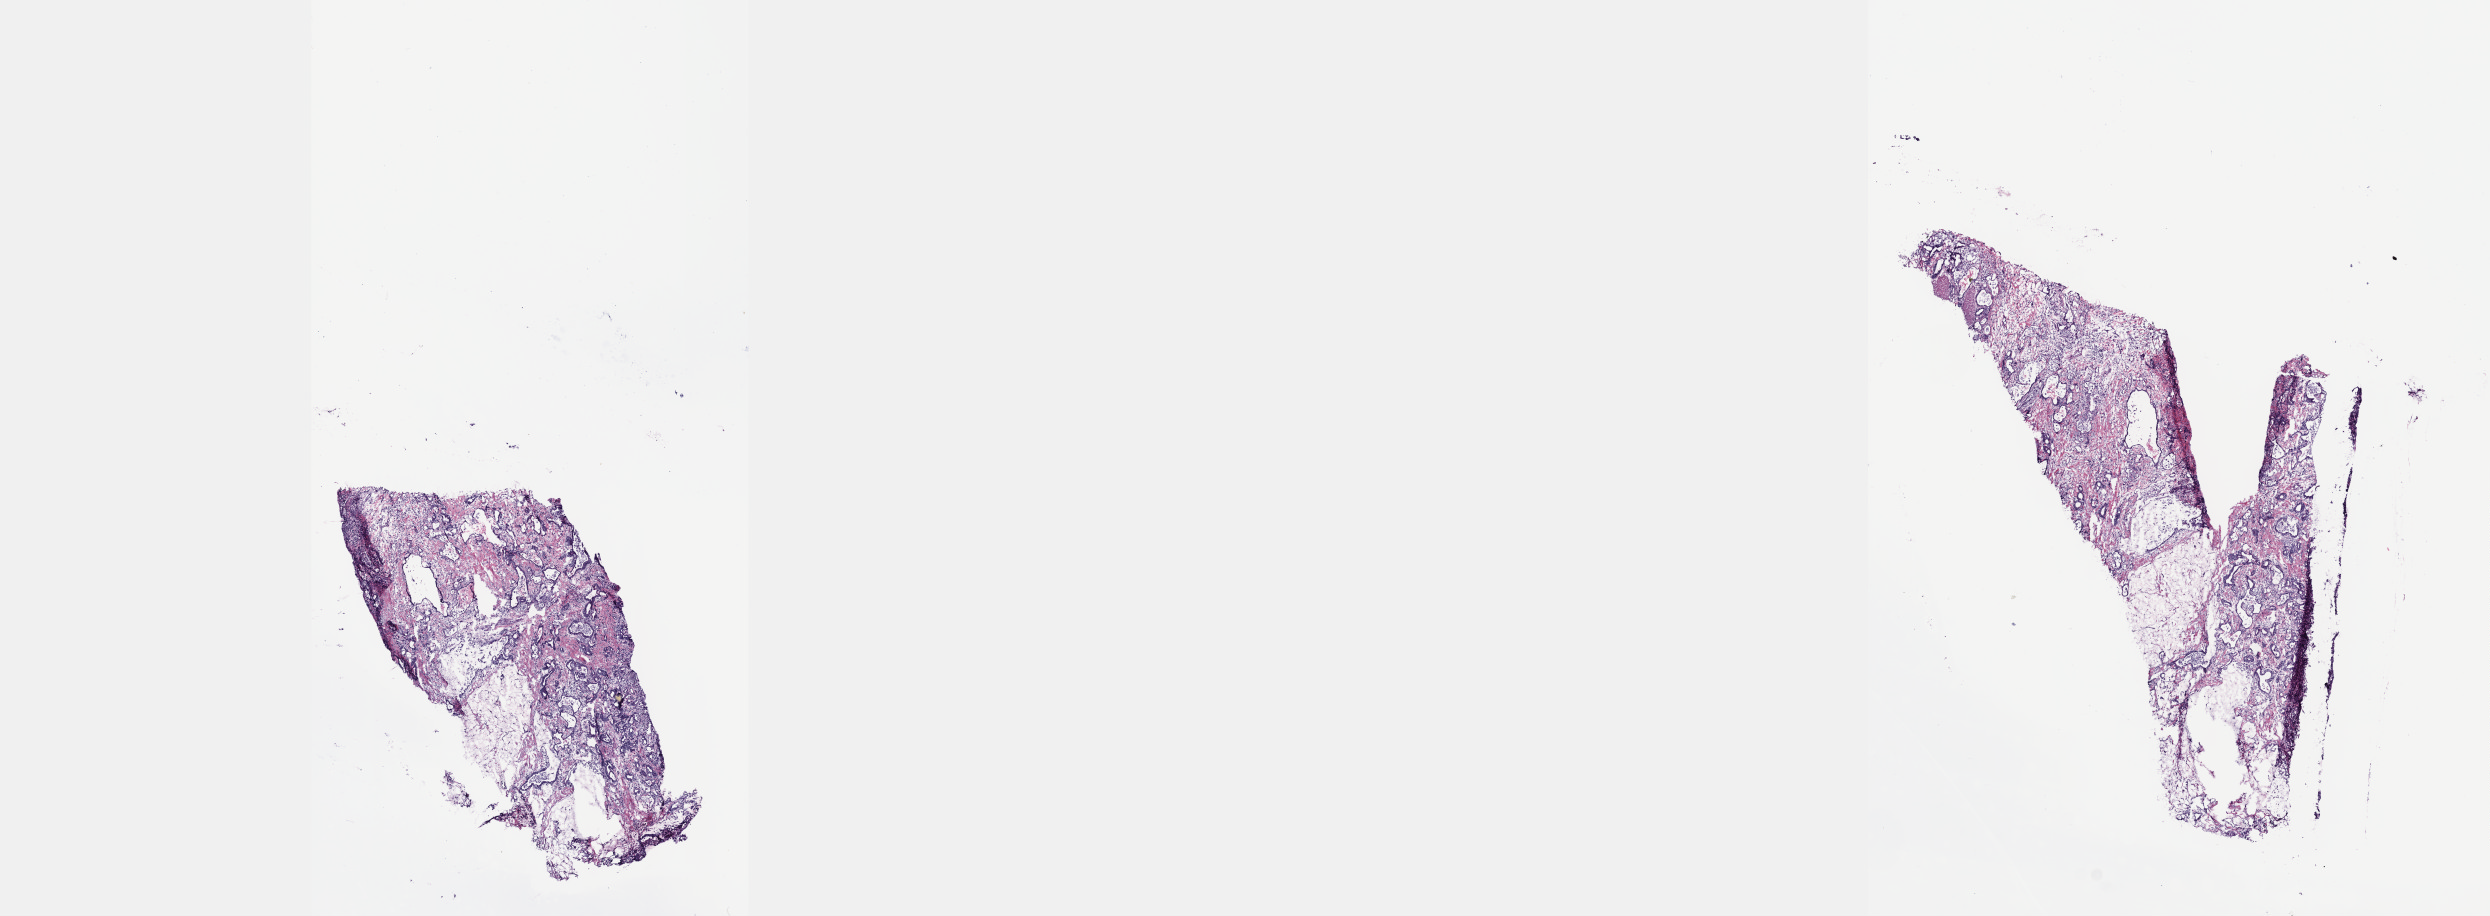
Whole-slide histology image, H&E-stained, whole scanned area (about 20.1 x 7.4 mm) shown as a low-resolution overview. Frozen section. Sample: primary tumour, stomach. Male patient; age at initial diagnosis 71 years. Histologic grade: G2 (moderately differentiated). Composition of this section per pathologist review: tumour cells 47%, tumour nuclei 80%, normal cells 0%, stromal cells 50%, necrosis 3%. Inflammatory infiltration, as recorded: lymphocyte infiltration 14%, monocyte infiltration 2%, neutrophil infiltration 2%.
AJCC pathologic stage: IB. Diagnosis: Adenocarcinoma, intestinal type (gastric antrum).